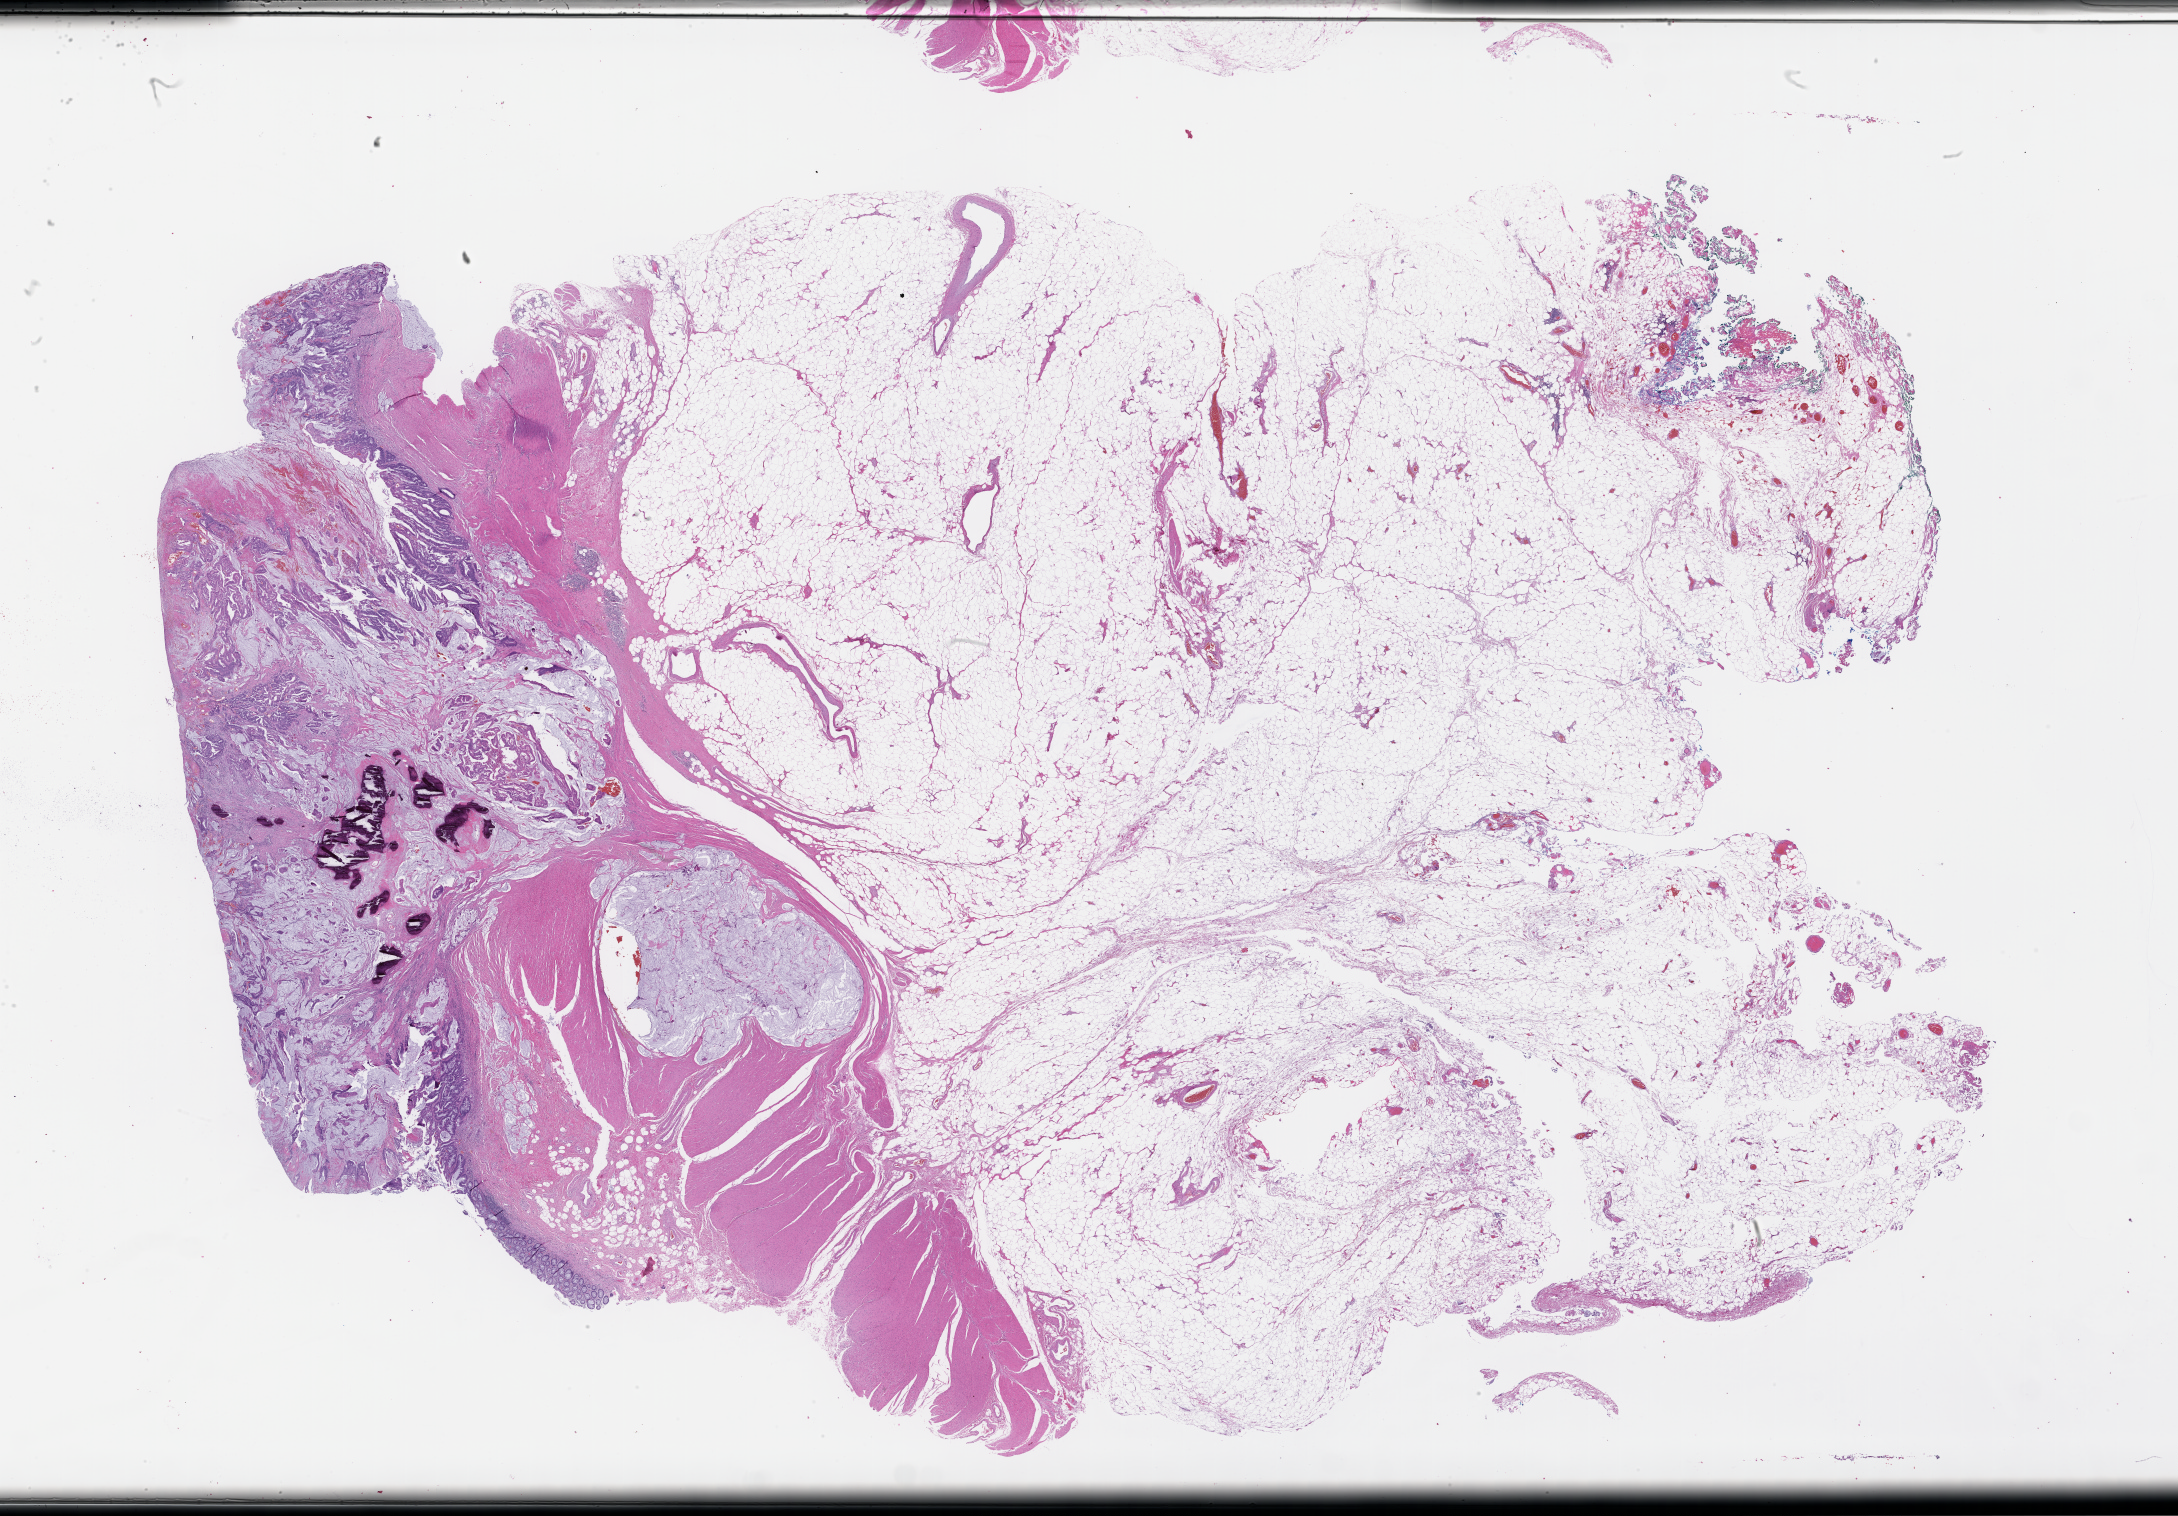
Digitized hematoxylin and eosin (H&E)-stained section, a low-resolution overview of the entire scanned area, about 35.2 x 24.5 mm, formalin-fixed, paraffin-embedded (FFPE) tissue, tissue site: rectum. Patient sex: male.
This section: primary tumour tissue. Diagnosis: Colorectal Carcinoma.